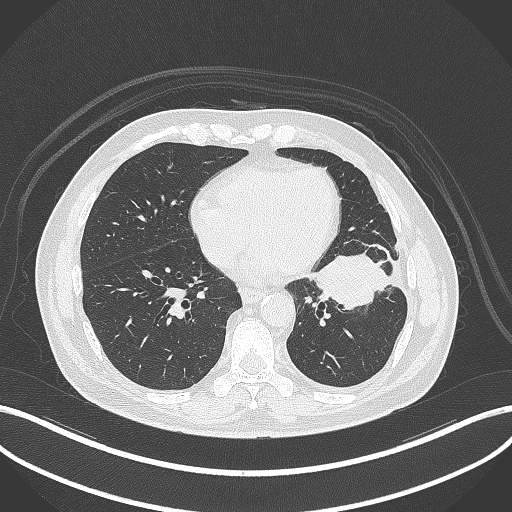
Chest CT, one axial slice; position 134 of 230 along the scan axis; 120 kVp; lung window (W 1500 / L -600 HU); 1 mm slice thickness; 512 × 512 image matrix, field of view 400 × 400 mm. Male patient, age 68 years. From the clinical record (not read from this slice): clinical TNM (as recorded): T2b N0 M0.
Annotated regions visible in this slice (rectangle marked by the reading radiologist):
- lung tumour (recorded histology: squamous cell carcinoma): bounding box [x1, y1, x2, y2] px = [310, 245, 394, 314]